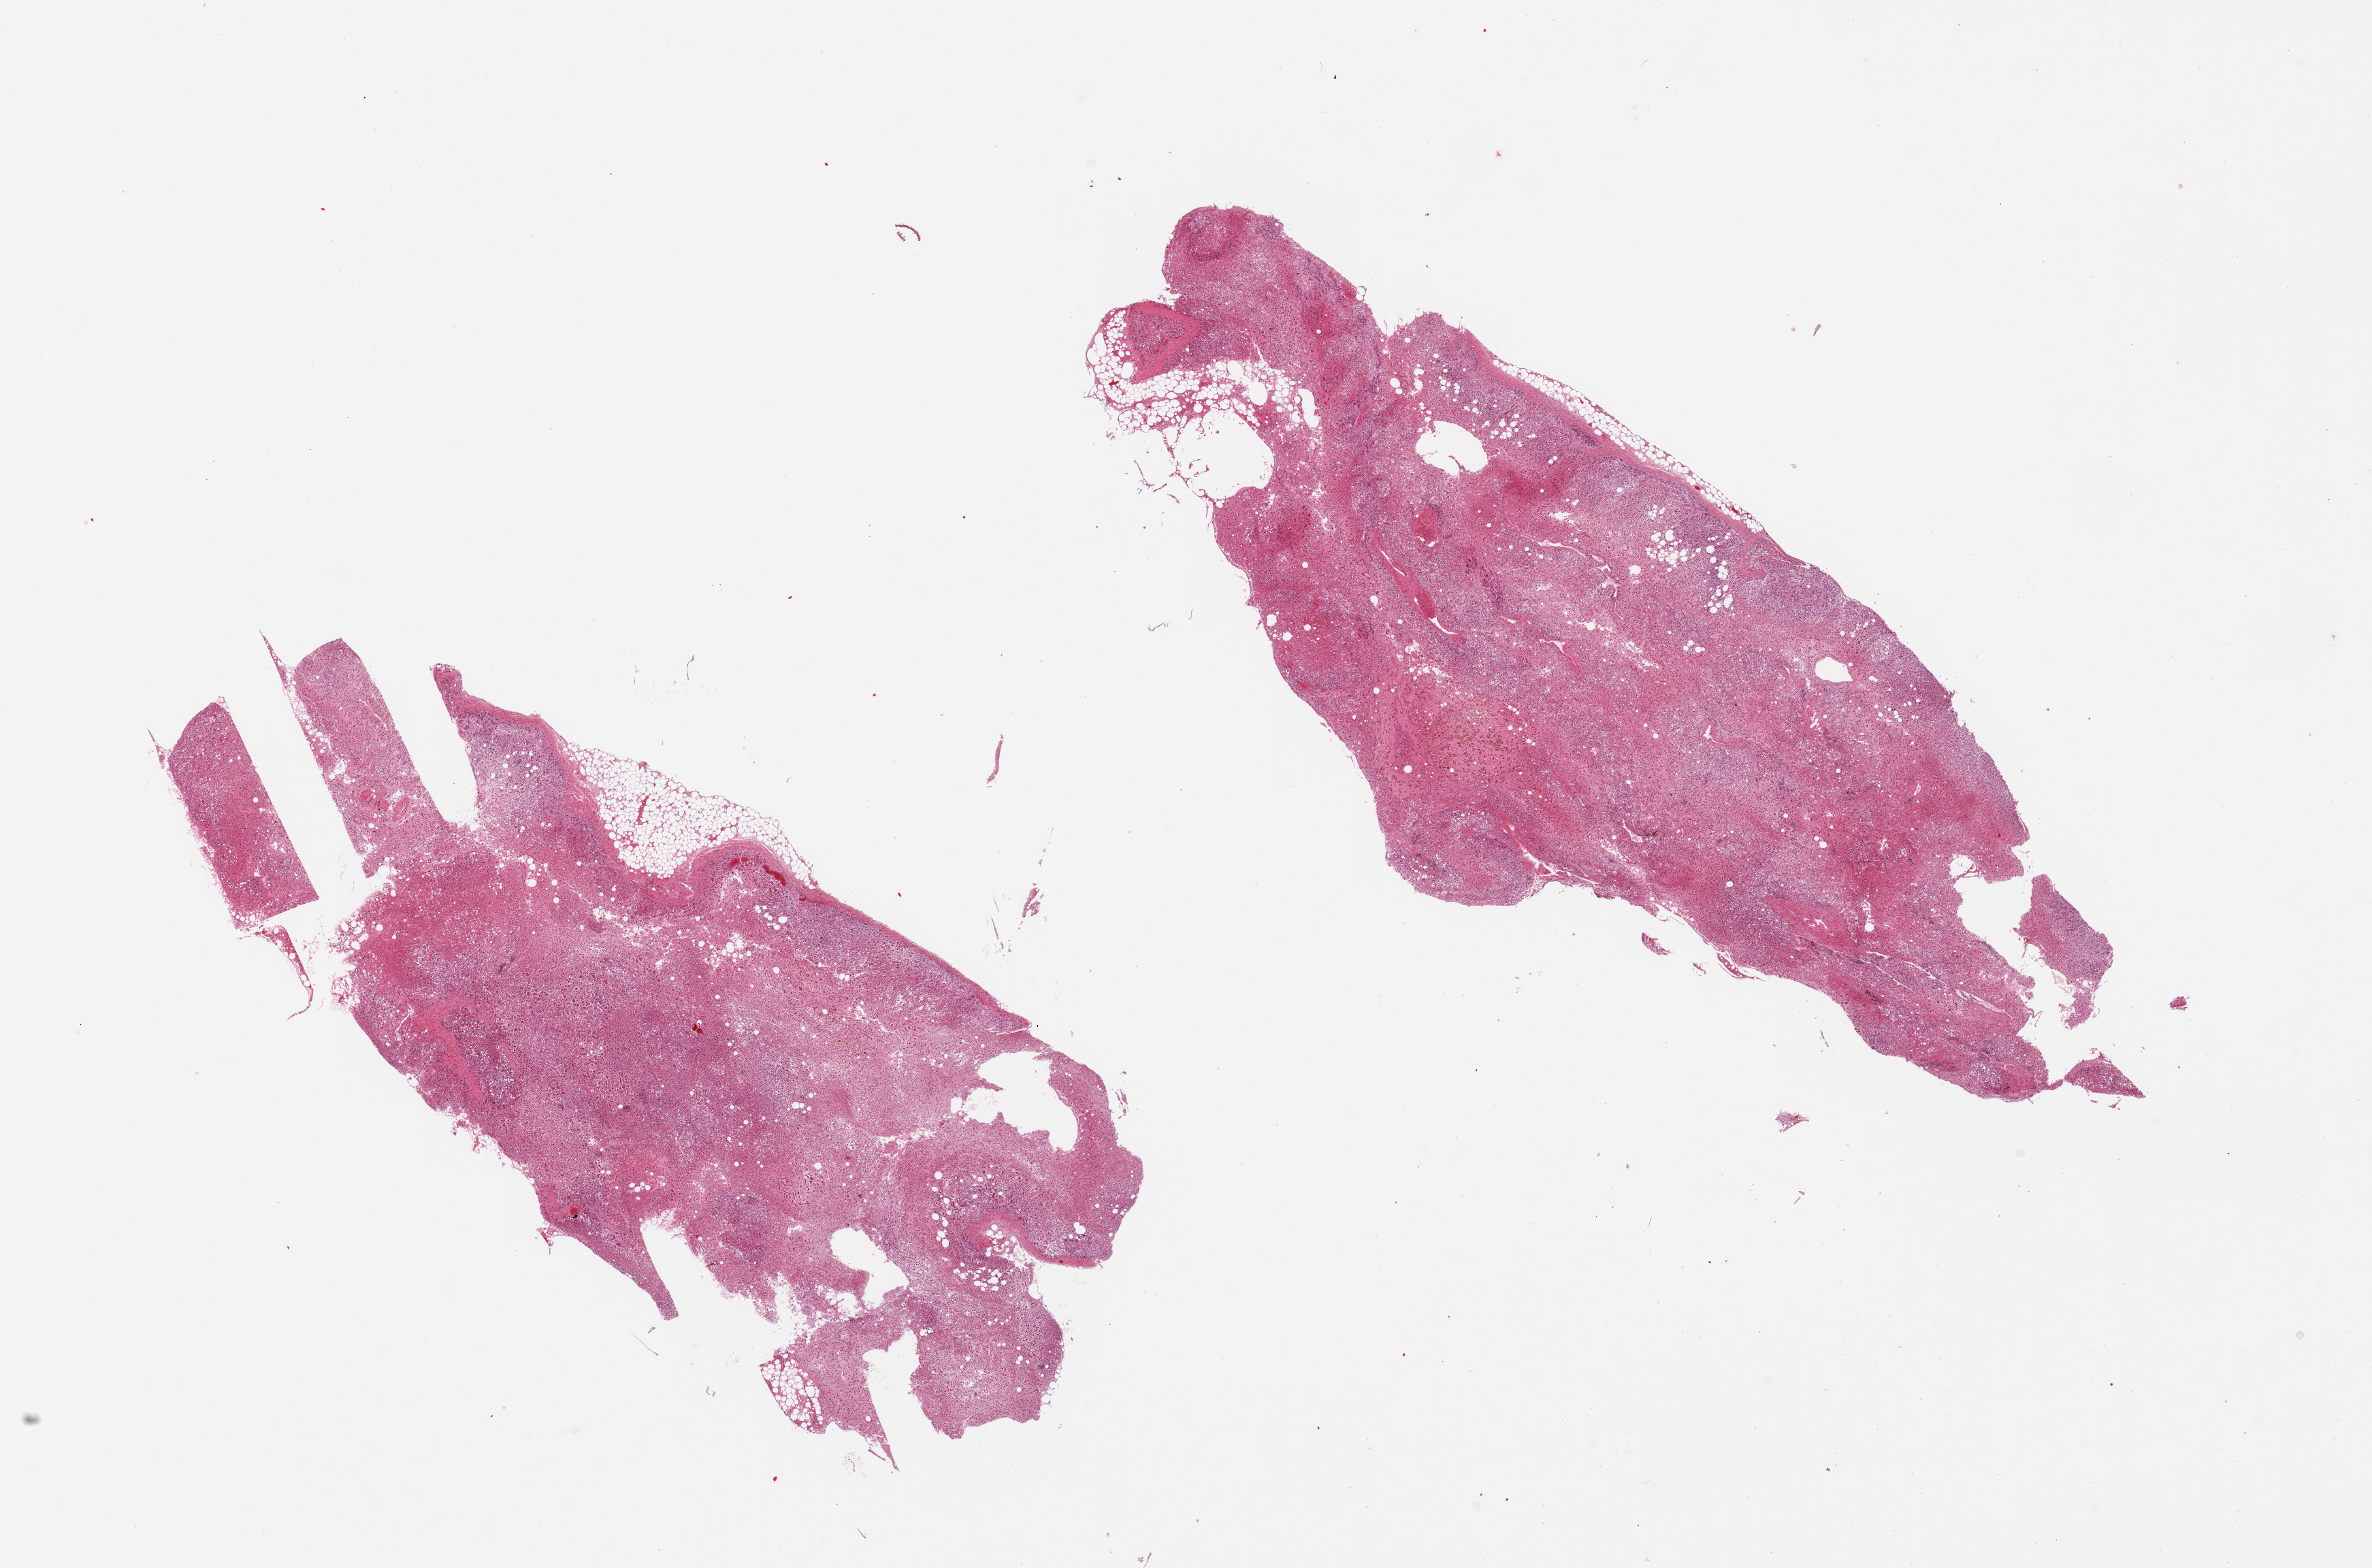
Whole-slide image, haematoxylin and eosin stain, low-resolution overview of the scanned area, about 27.6 x 18.2 mm (from a 20x scan); PAXgene-fixed paraffin-embedded (PFPE) section; section of adrenal gland (target tissue); donor tissue sample.
Reviewer comment on this tissue sample: 2 pieces.